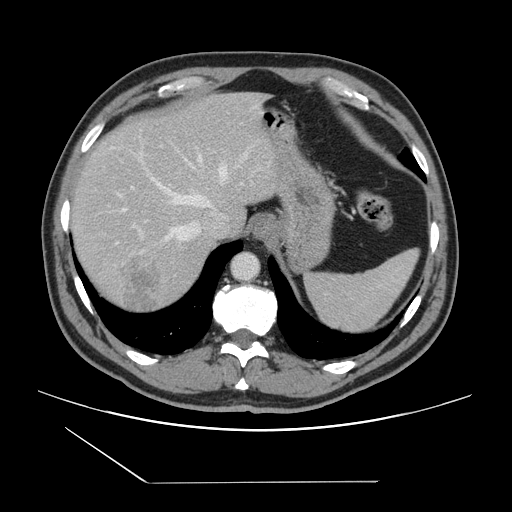
Contrast-enhanced abdominal CT, one axial slice; position 117 of 157 along the scan axis; intravenous contrast given; soft-tissue window (W 400 / L 40 HU); 2.5 mm slice thickness; 512 × 512 image matrix, field of view 407 × 407 mm. Male patient, age 61 years. From the clinical record (not read from this slice): diagnosis: colorectal cancer liver metastases, imaged before liver resection; multiple liver metastases: yes; largest metastasis: 5.5 cm.
Structures marked on this image (manually delineated by an expert):
- hepatic veins: box from (x=123, y=153) to (x=246, y=254) px
- liver: (x=70, y=93)–(x=279, y=313)
- planned liver remnant (the part of the liver to remain after resection): (x=72, y=93)–(x=235, y=232)
- portal vein (with intrahepatic branches): (x=116, y=187)–(x=143, y=243)
- liver metastasis: (x=119, y=255)–(x=162, y=314)